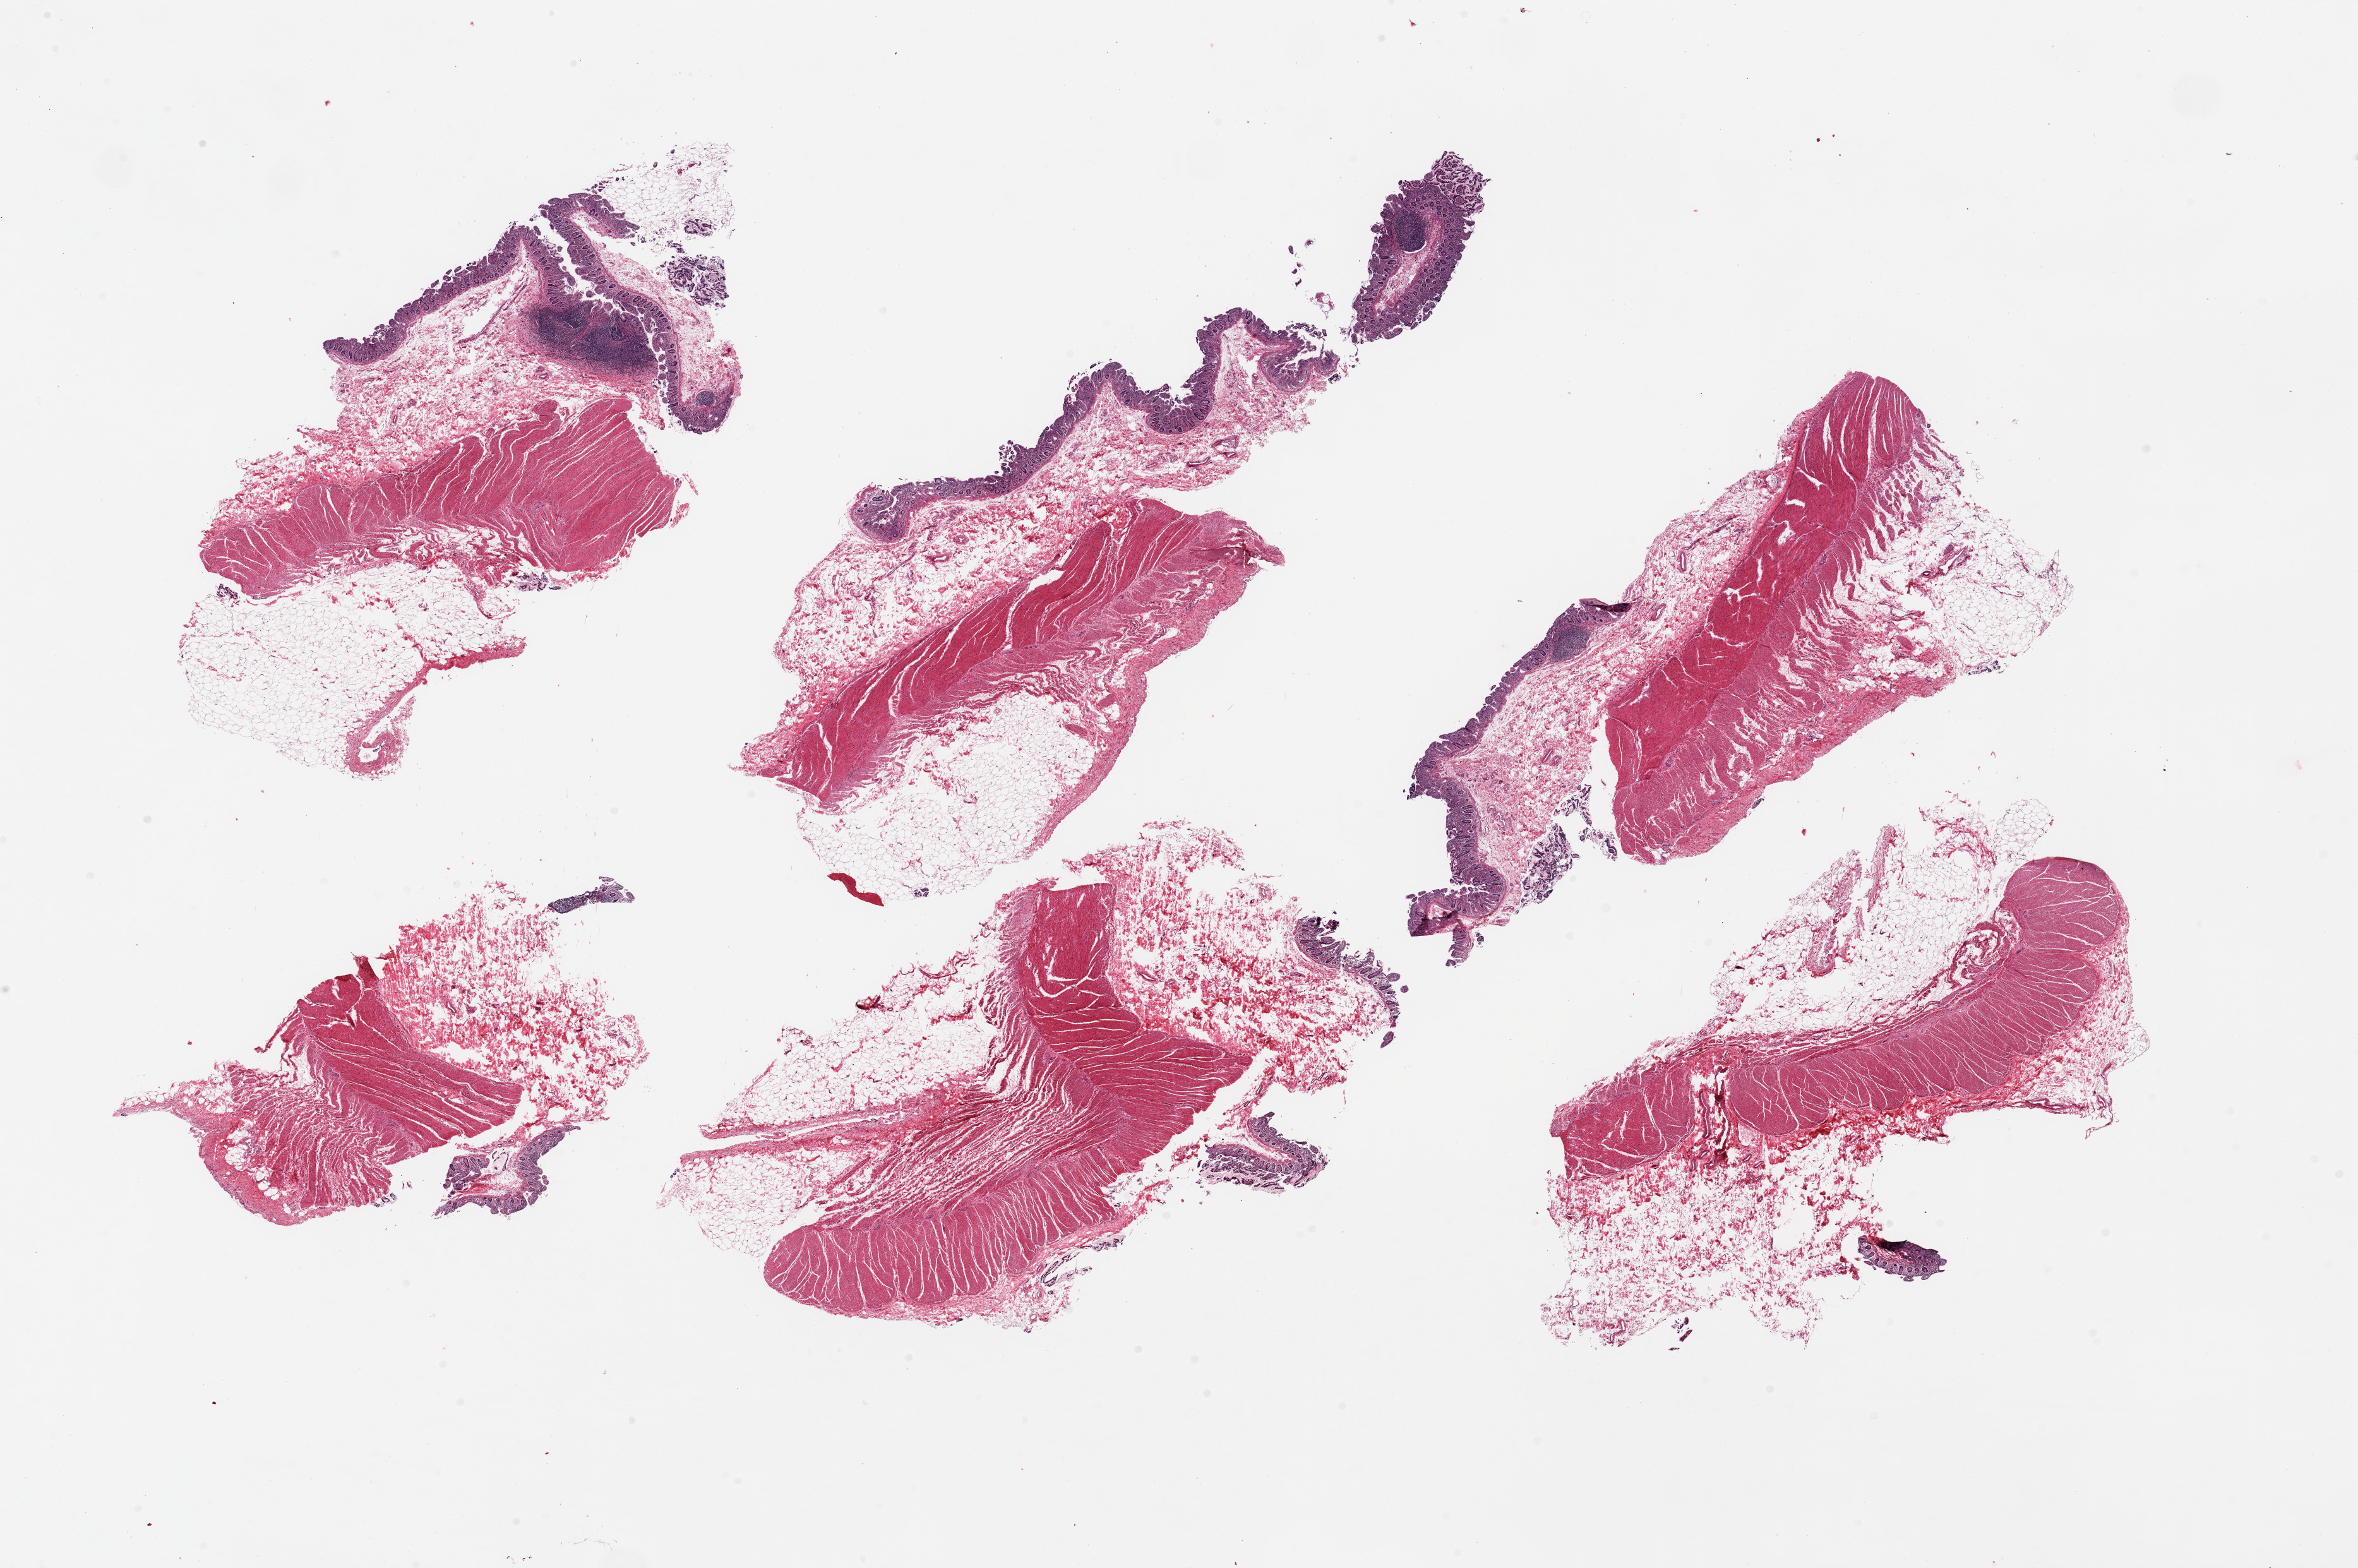
Haematoxylin and eosin whole-slide image, brightfield — whole scanned area (about 29.5 x 19.6 mm) shown as a low-resolution overview.
Specimen: PAXgene-fixed paraffin-embedded (PFPE) section; section of ileum (target tissue); tissue donor sample.